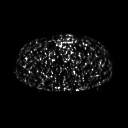
FDG PET of an extremity soft-tissue mass (from a PET/CT study), one axial slice; slice 267 of 267 in the series (ordered by position); 3.27 mm slice thickness; 128 × 128 image matrix, field of view 500 × 500 mm. Male patient, age 27 years. Case-level facts recorded for this patient, not image findings: histological type: extraskeletal osteosarcoma; grade: high; site of the primary tumour: left adductur.
Outlined on this slice (expert contour drawn on MRI and transferred to this co-registered scan by the dataset authors):
- gross tumour volume (mass): bounding box <76,49,96,74> (left, top, right, bottom; pixels)